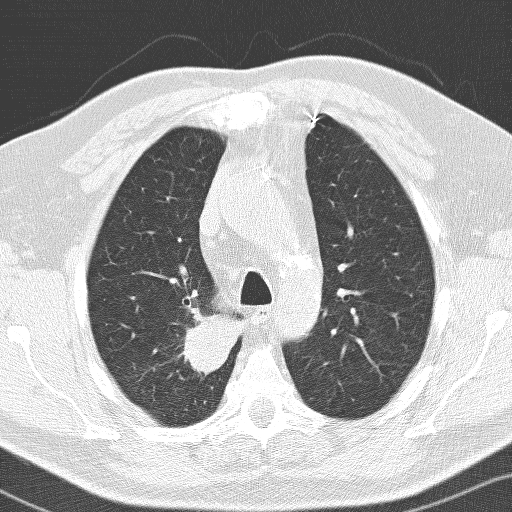
Low-dose screening chest CT, one axial slice. 120 kVp. Lung window (W 1500 / L -600 HU). 512 × 512 image matrix, field of view 326 × 326 mm.
Annotated regions visible in this slice (manually delineated by an expert):
- lesion 1 (tumor, upper lobe of right lung): bounding box <181,308,244,375> (left, top, right, bottom; pixels)